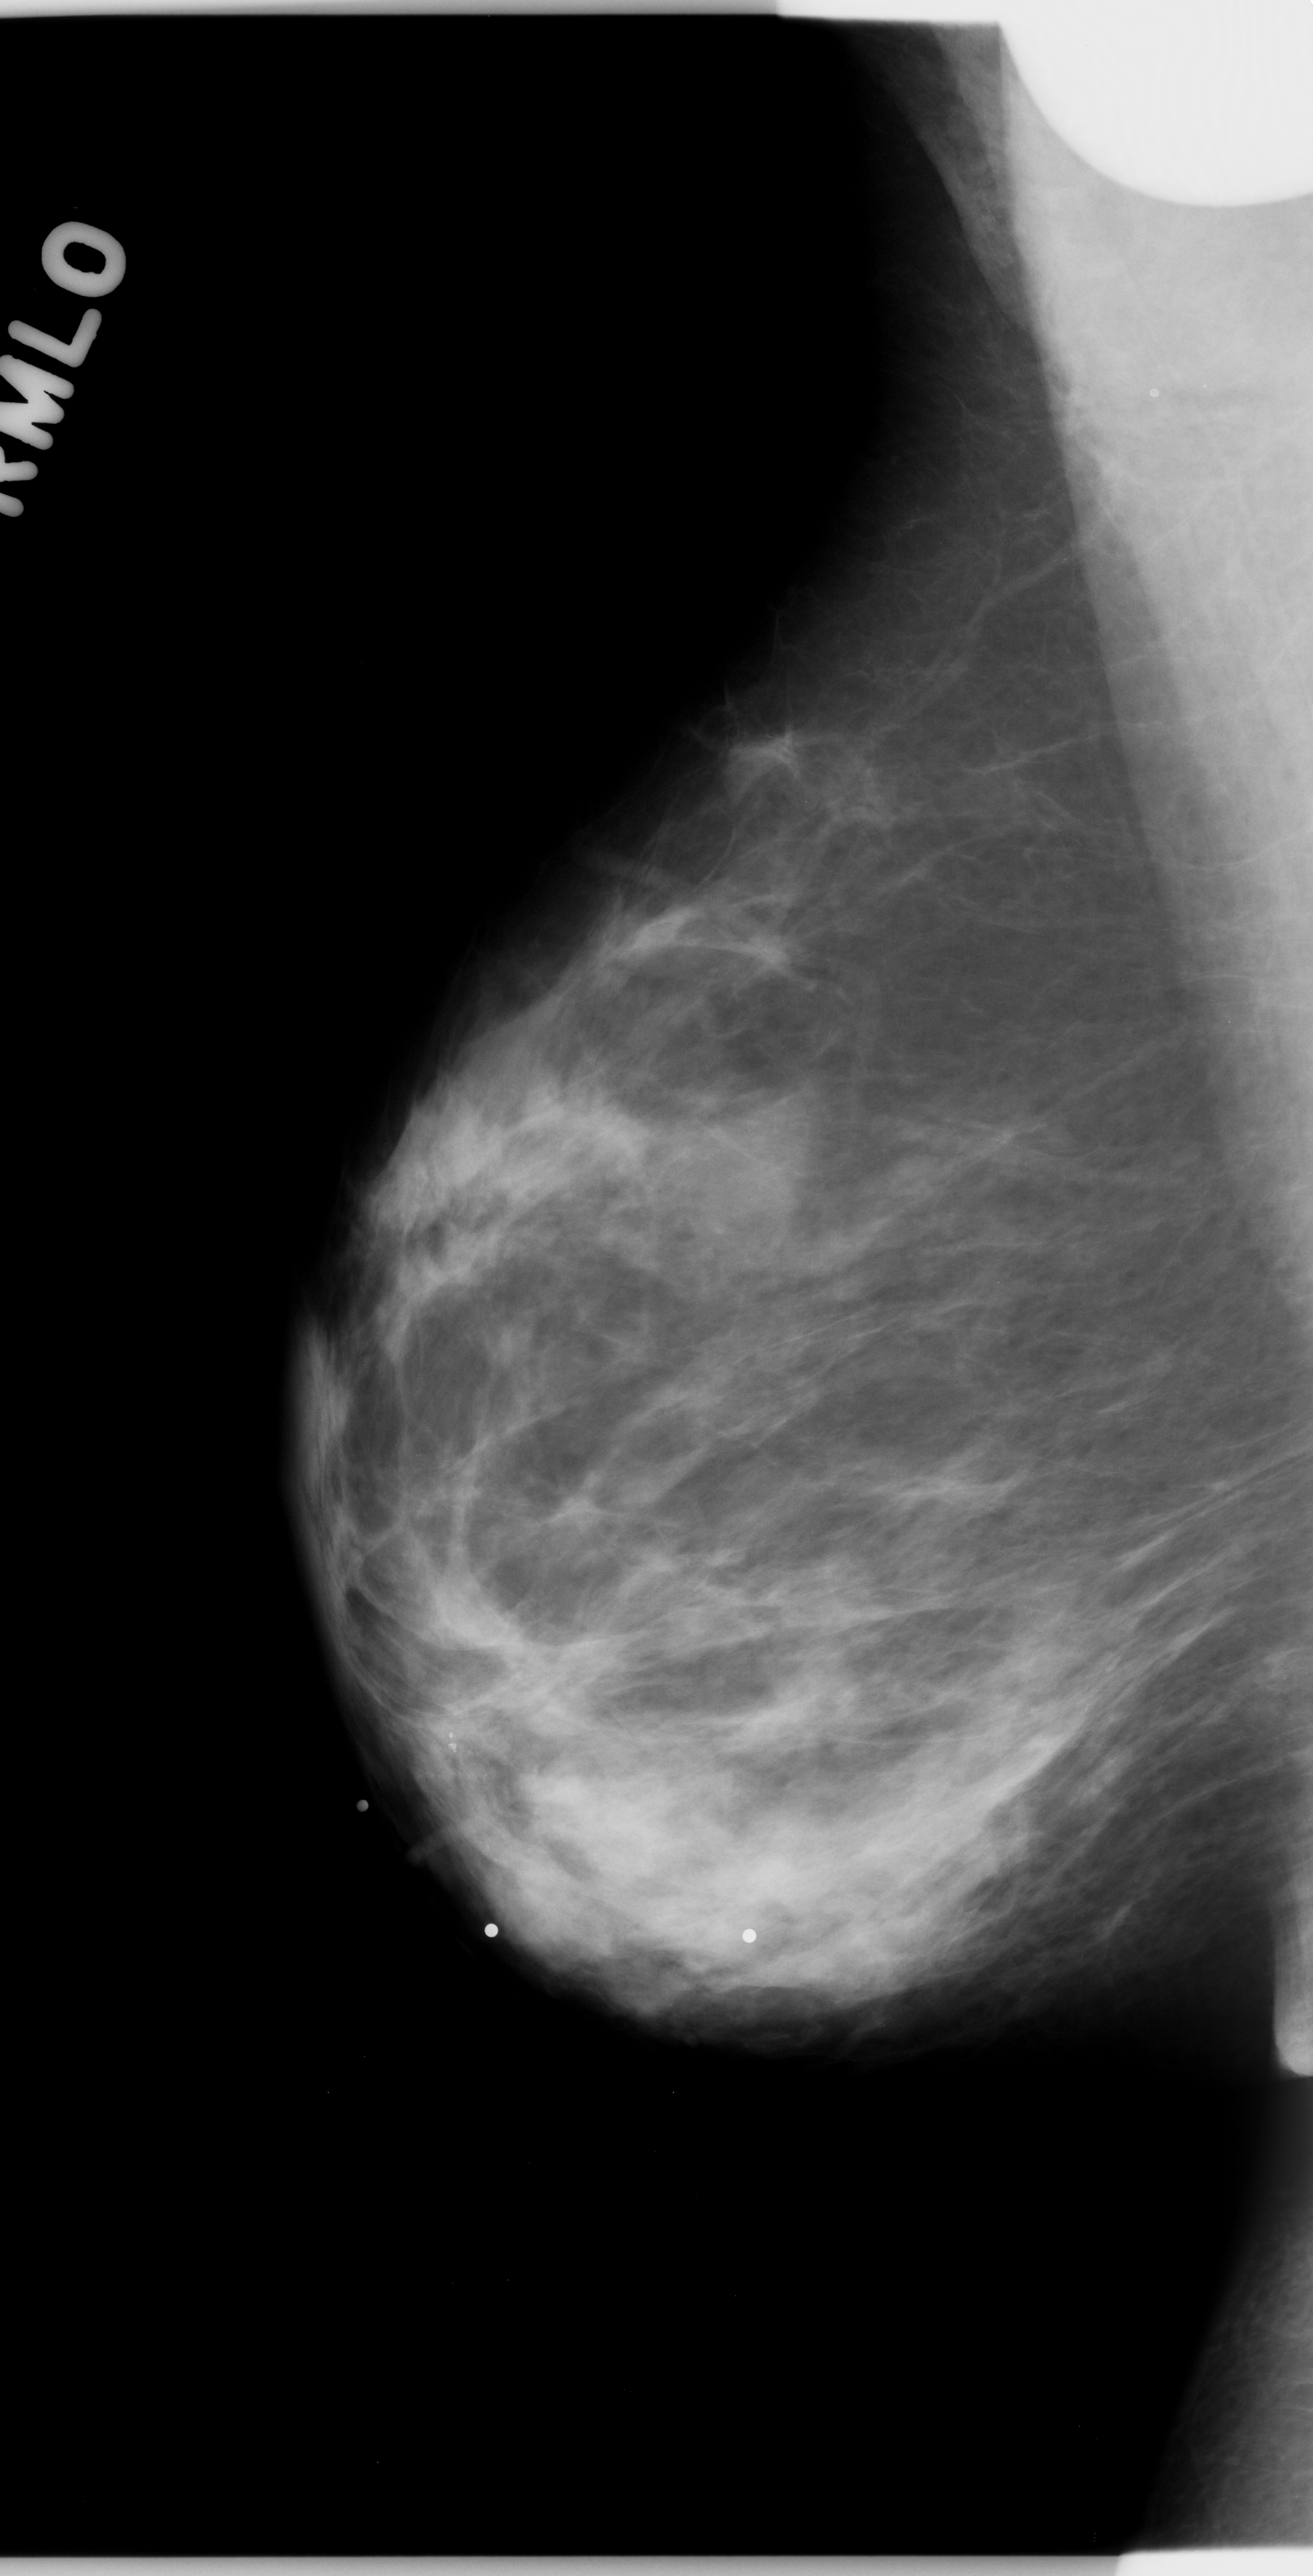
Mammogram (digitized film). Right breast. MLO view. 1313 × 2576 image matrix.
Expert-marked regions of interest on this film, with their recorded descriptors:
- mass, shape oval, margins obscured; BI-RADS assessment category 4; pathology result (as recorded, not read from the image): malignant: bounding box <480,1832,603,1956> (left, top, right, bottom; pixels)